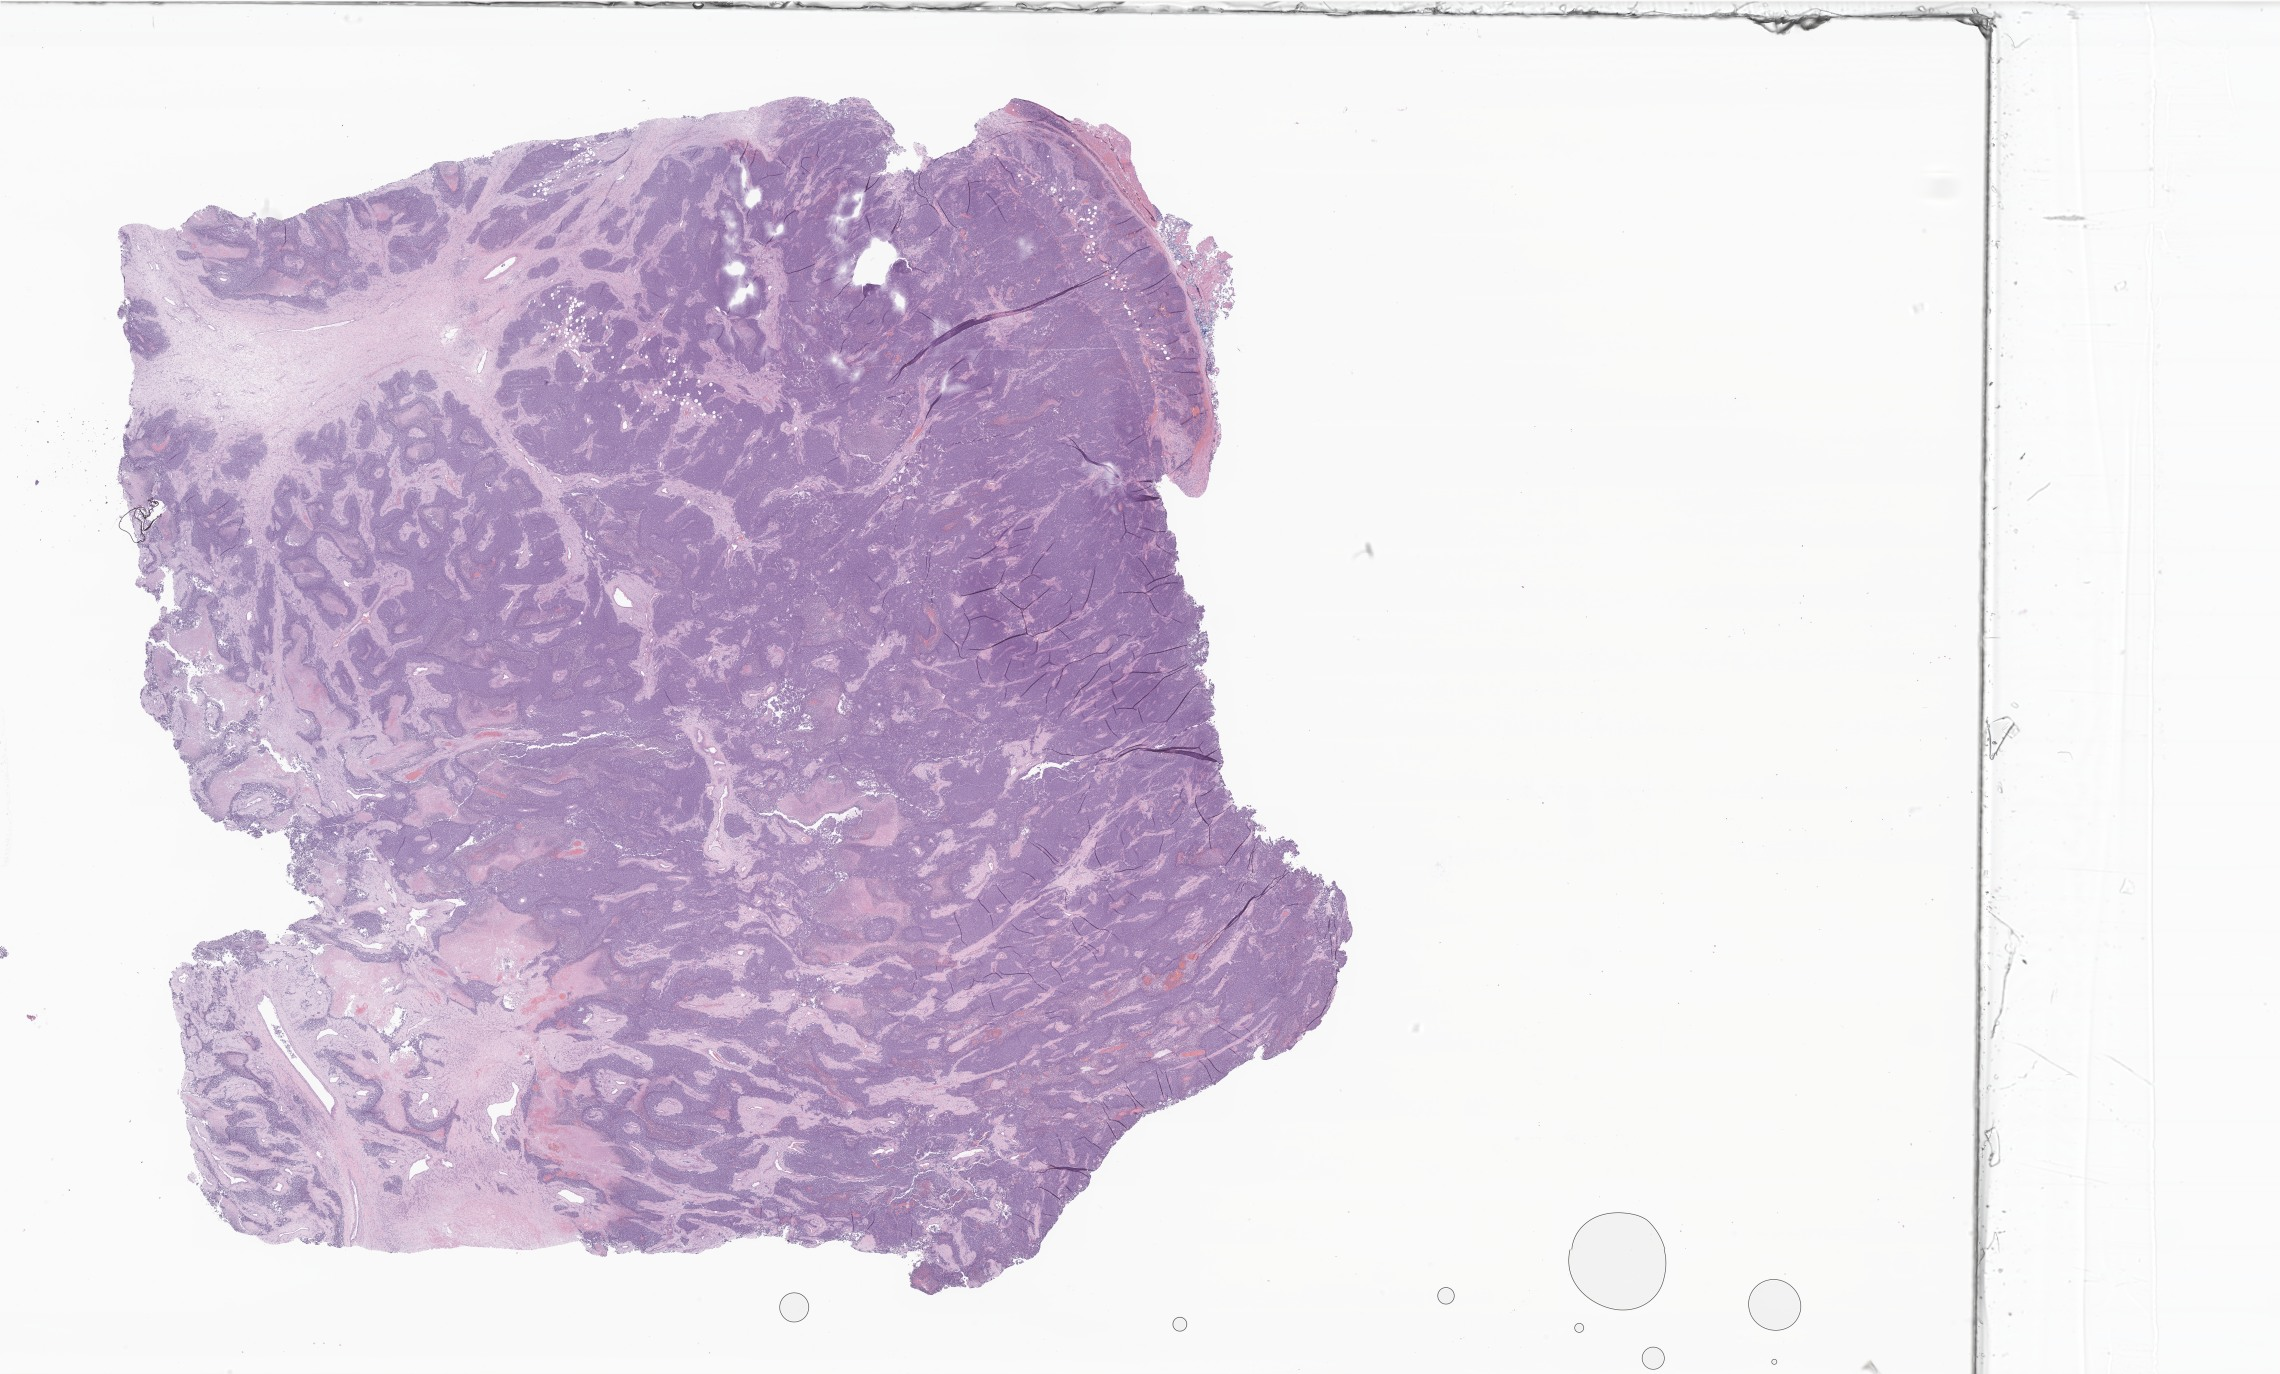
Whole-slide image, hematoxylin and eosin (H&E) stain of tumor tissue from the kidney, a low-resolution overview of the entire scanned area, about 38.5 x 23.2 mm. Male patient, age 164 months.
Specimen: formalin-fixed, paraffin-embedded (FFPE) tissue.